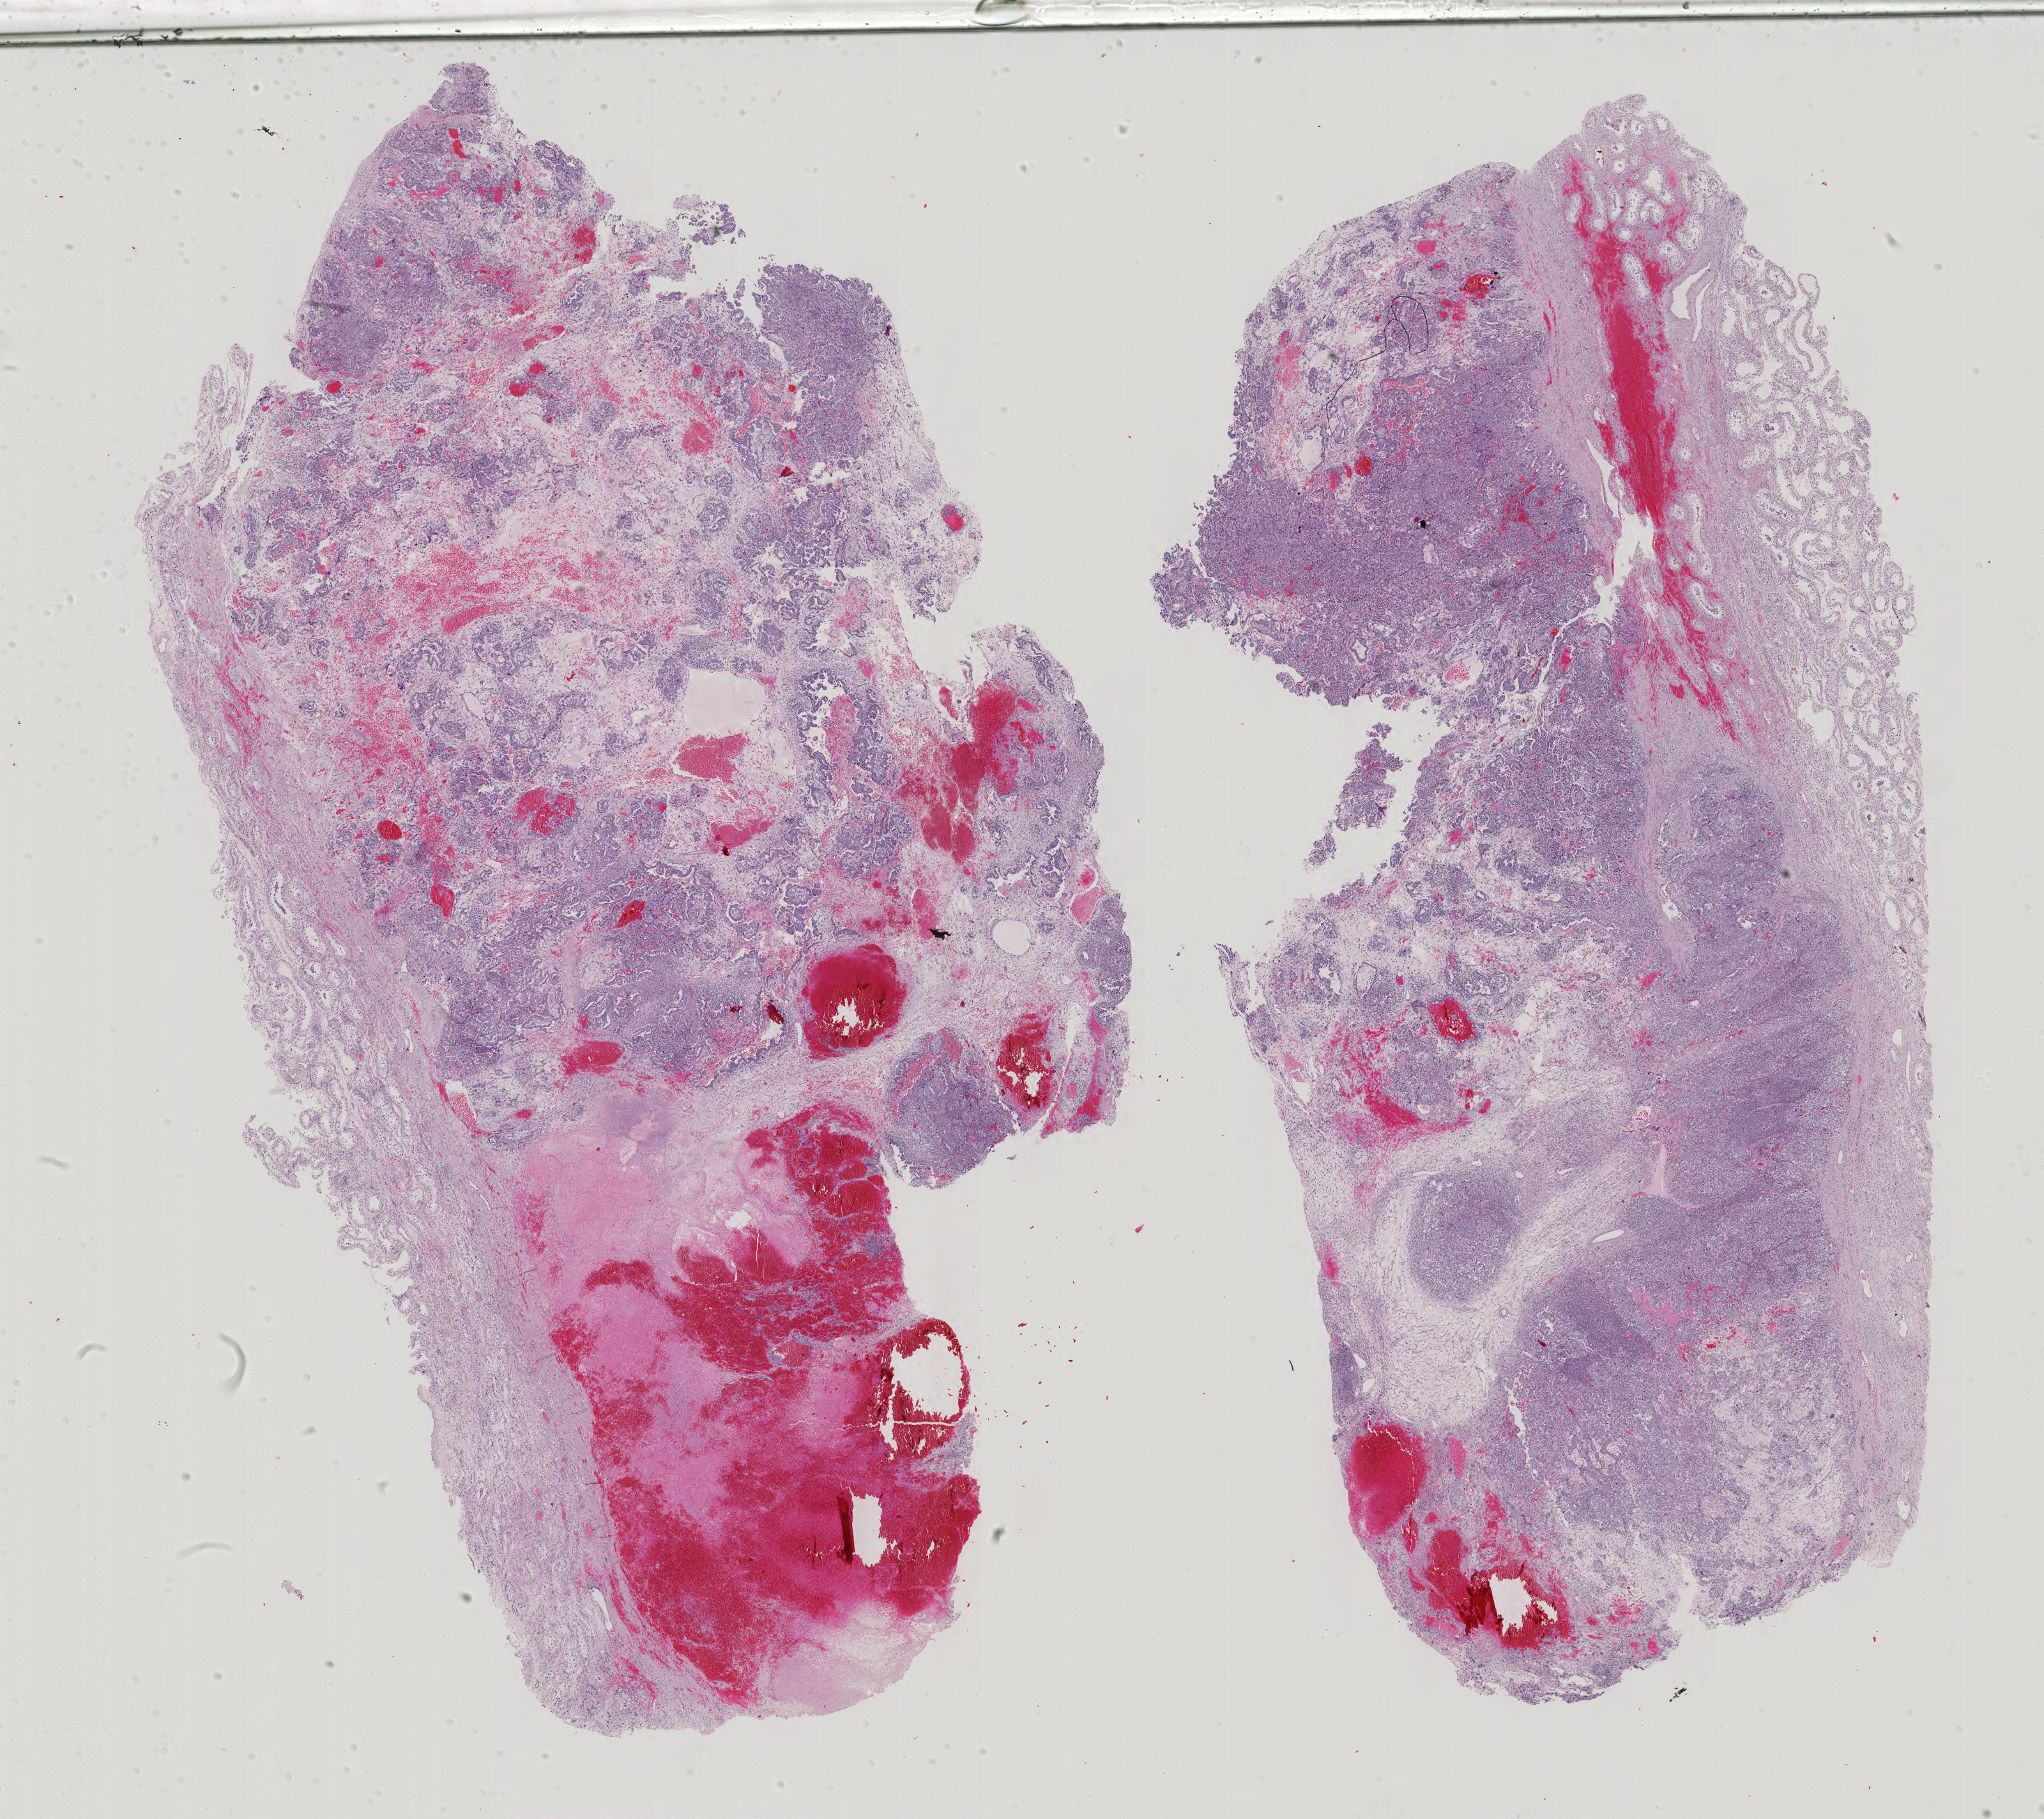
Whole-slide histology image, H&E-stained, whole scanned area (about 23.3 x 20.8 mm, slide scanned at 40x) shown as a low-resolution overview, formalin-fixed paraffin-embedded (FFPE) diagnostic section, testis, primary tumour sample. Male, age 41 years at initial diagnosis.
Diagnosis: Embryonal carcinoma, NOS. TNM: T2 N0 M0. AJCC pathologic stage: IB (7th edition). Laterality: left.